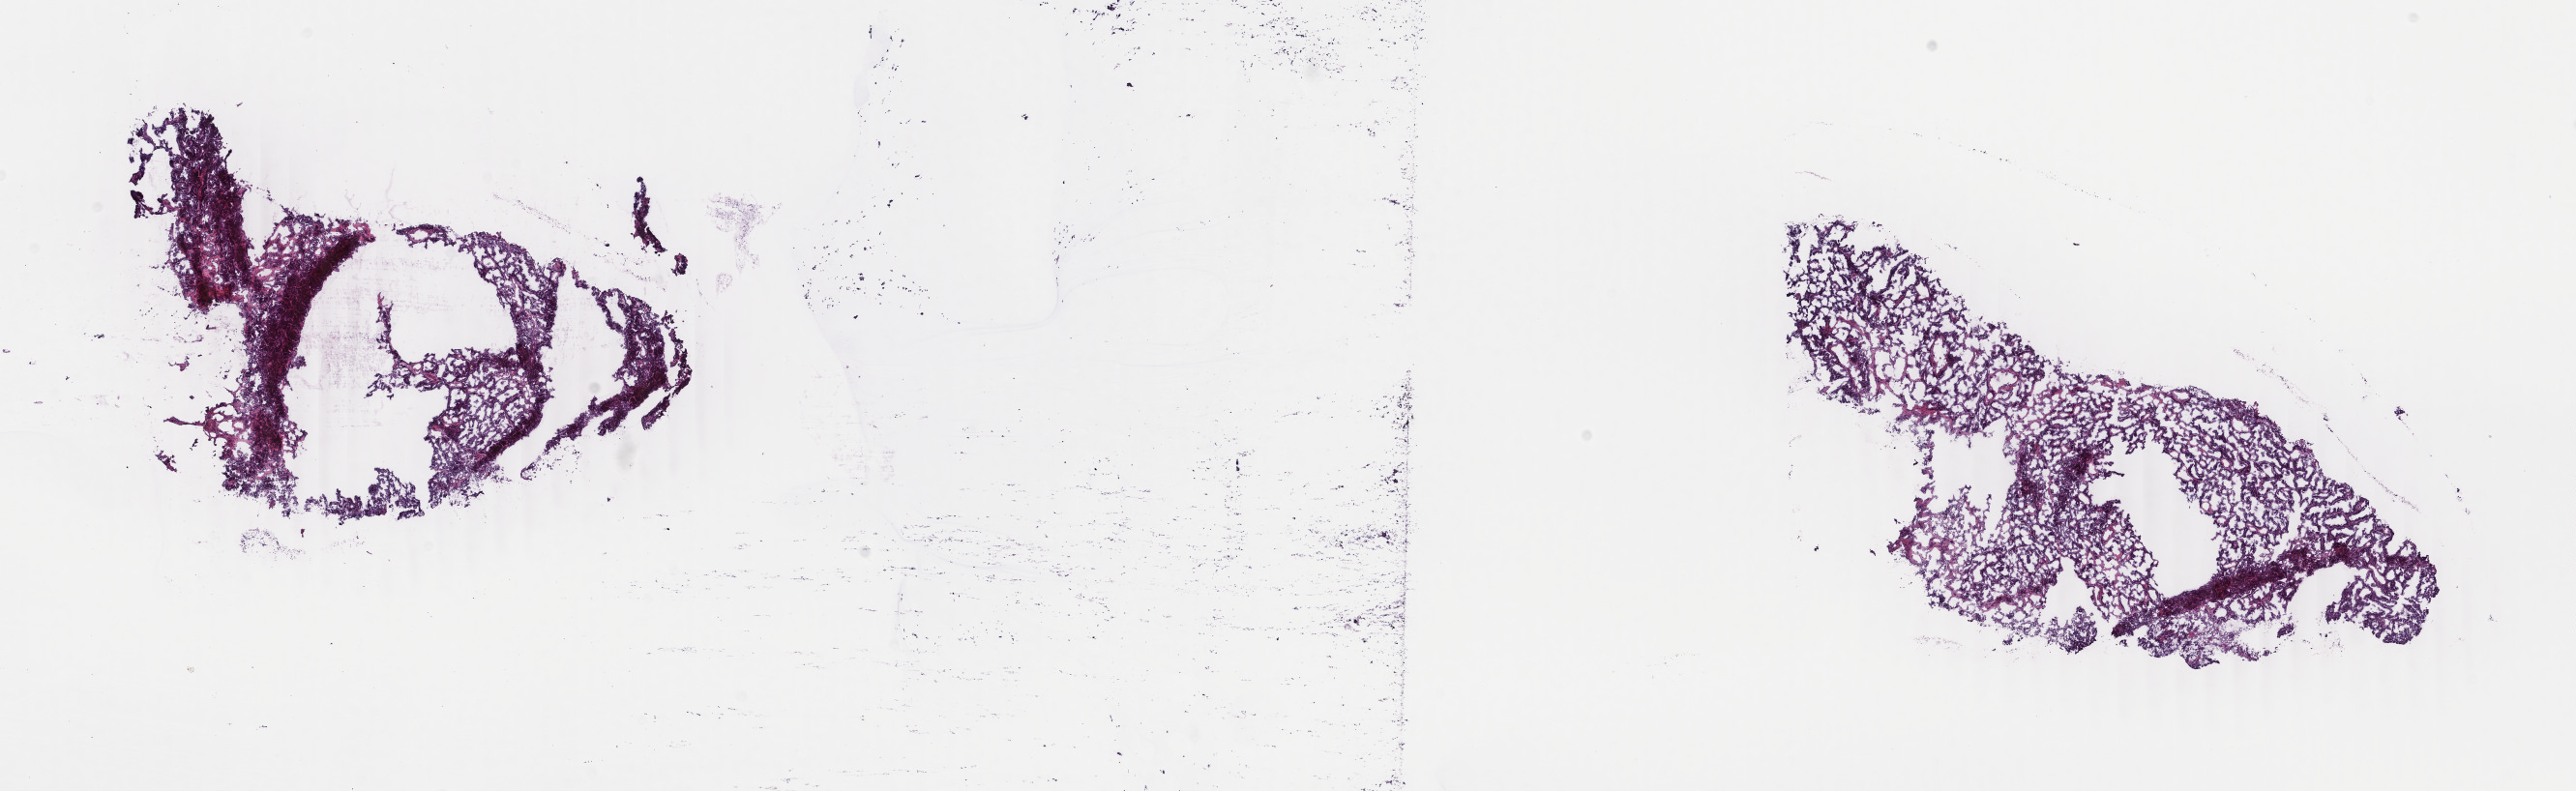
Whole-slide histology image, Hematoxylin and eosin (H&E) stained, low-resolution overview of the scanned area, about 21.2 x 6.5 mm (acquisition: 40x scan), frozen section from the top of the tissue portion, primary tumour sample from the uterus. Female, age 76 years at initial diagnosis. Histologic grade: high grade. Pathologist review of this section (percent, as recorded): tumour cells 70%, tumour nuclei 70%, normal cells 0%, stromal cells 10%, necrosis 20%. Infiltration values recorded for this section: lymphocyte infiltration 40%, monocyte infiltration 10%, neutrophil infiltration 40%.
Lymph nodes positive (case pathology): 2 of 21 examined. FIGO stage: IIIC. Histologic diagnosis: Serous cystadenocarcinoma, NOS (endometrium).